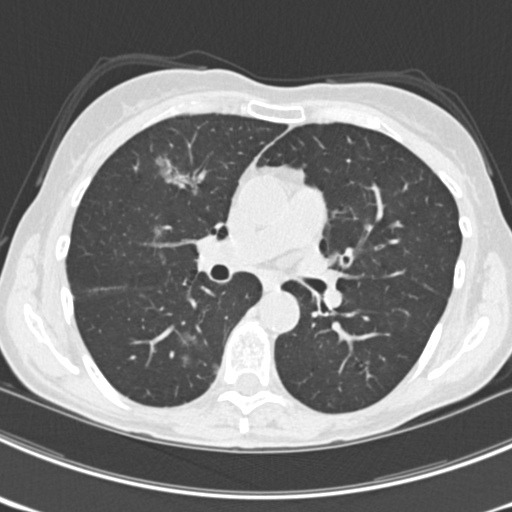
Axial slice from a low-dose chest CT screening exam. Third screening round (two years after baseline). Lung window (W 1500 / L -600 HU). 2 mm slice thickness. 120 kVp. 512 × 512 image matrix. Female, age 63 years at enrolment. Current smoker at enrolment.
Lesion marked by an expert reader, bounding box [x1, y1, x2, y2] px = [150, 143, 214, 201]. The screening reader recorded 9 non-calcified nodules or masses ≥4 mm on this exam (left upper lobe, right upper lobe, left upper lobe, left lower lobe, right middle lobe, left lower lobe, left lower lobe, right lower lobe, right lower lobe); which of them this box marks is not recorded. Lung cancer was diagnosed 15 days after this screen: bronchiolo-alveolar adenocarcinoma, NOS, right upper lobe, right middle lobe, right lower lobe, left upper lobe, left lower lobe, moderately differentiated (G2), stage IV (AJCC 6th edition).